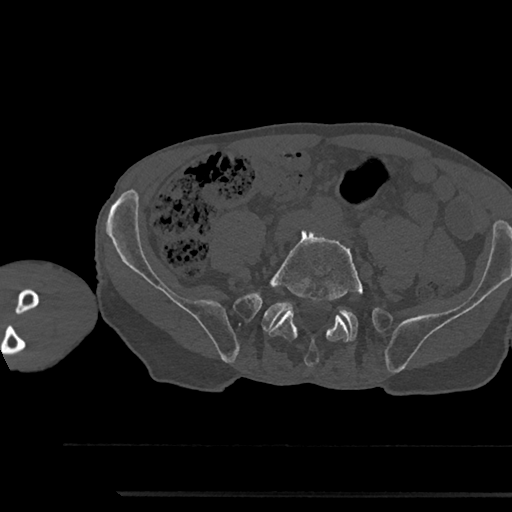
CT including the spine, one axial slice. Position 335 of 797 along the scan axis. Reconstruction kernel Br40s/3. Bone window (W 1800 / L 400 HU). 0.5 mm slice thickness. 512 × 512 image matrix. Male patient, age 79 years. Case-level facts recorded for this patient, not image findings: primary cancer: prostate.
Structures marked on this image (semi-automatic segmentation, software-assisted and operator-edited):
- L5 vertebra: bounding box <269,230,363,367> (left, top, right, bottom; pixels)